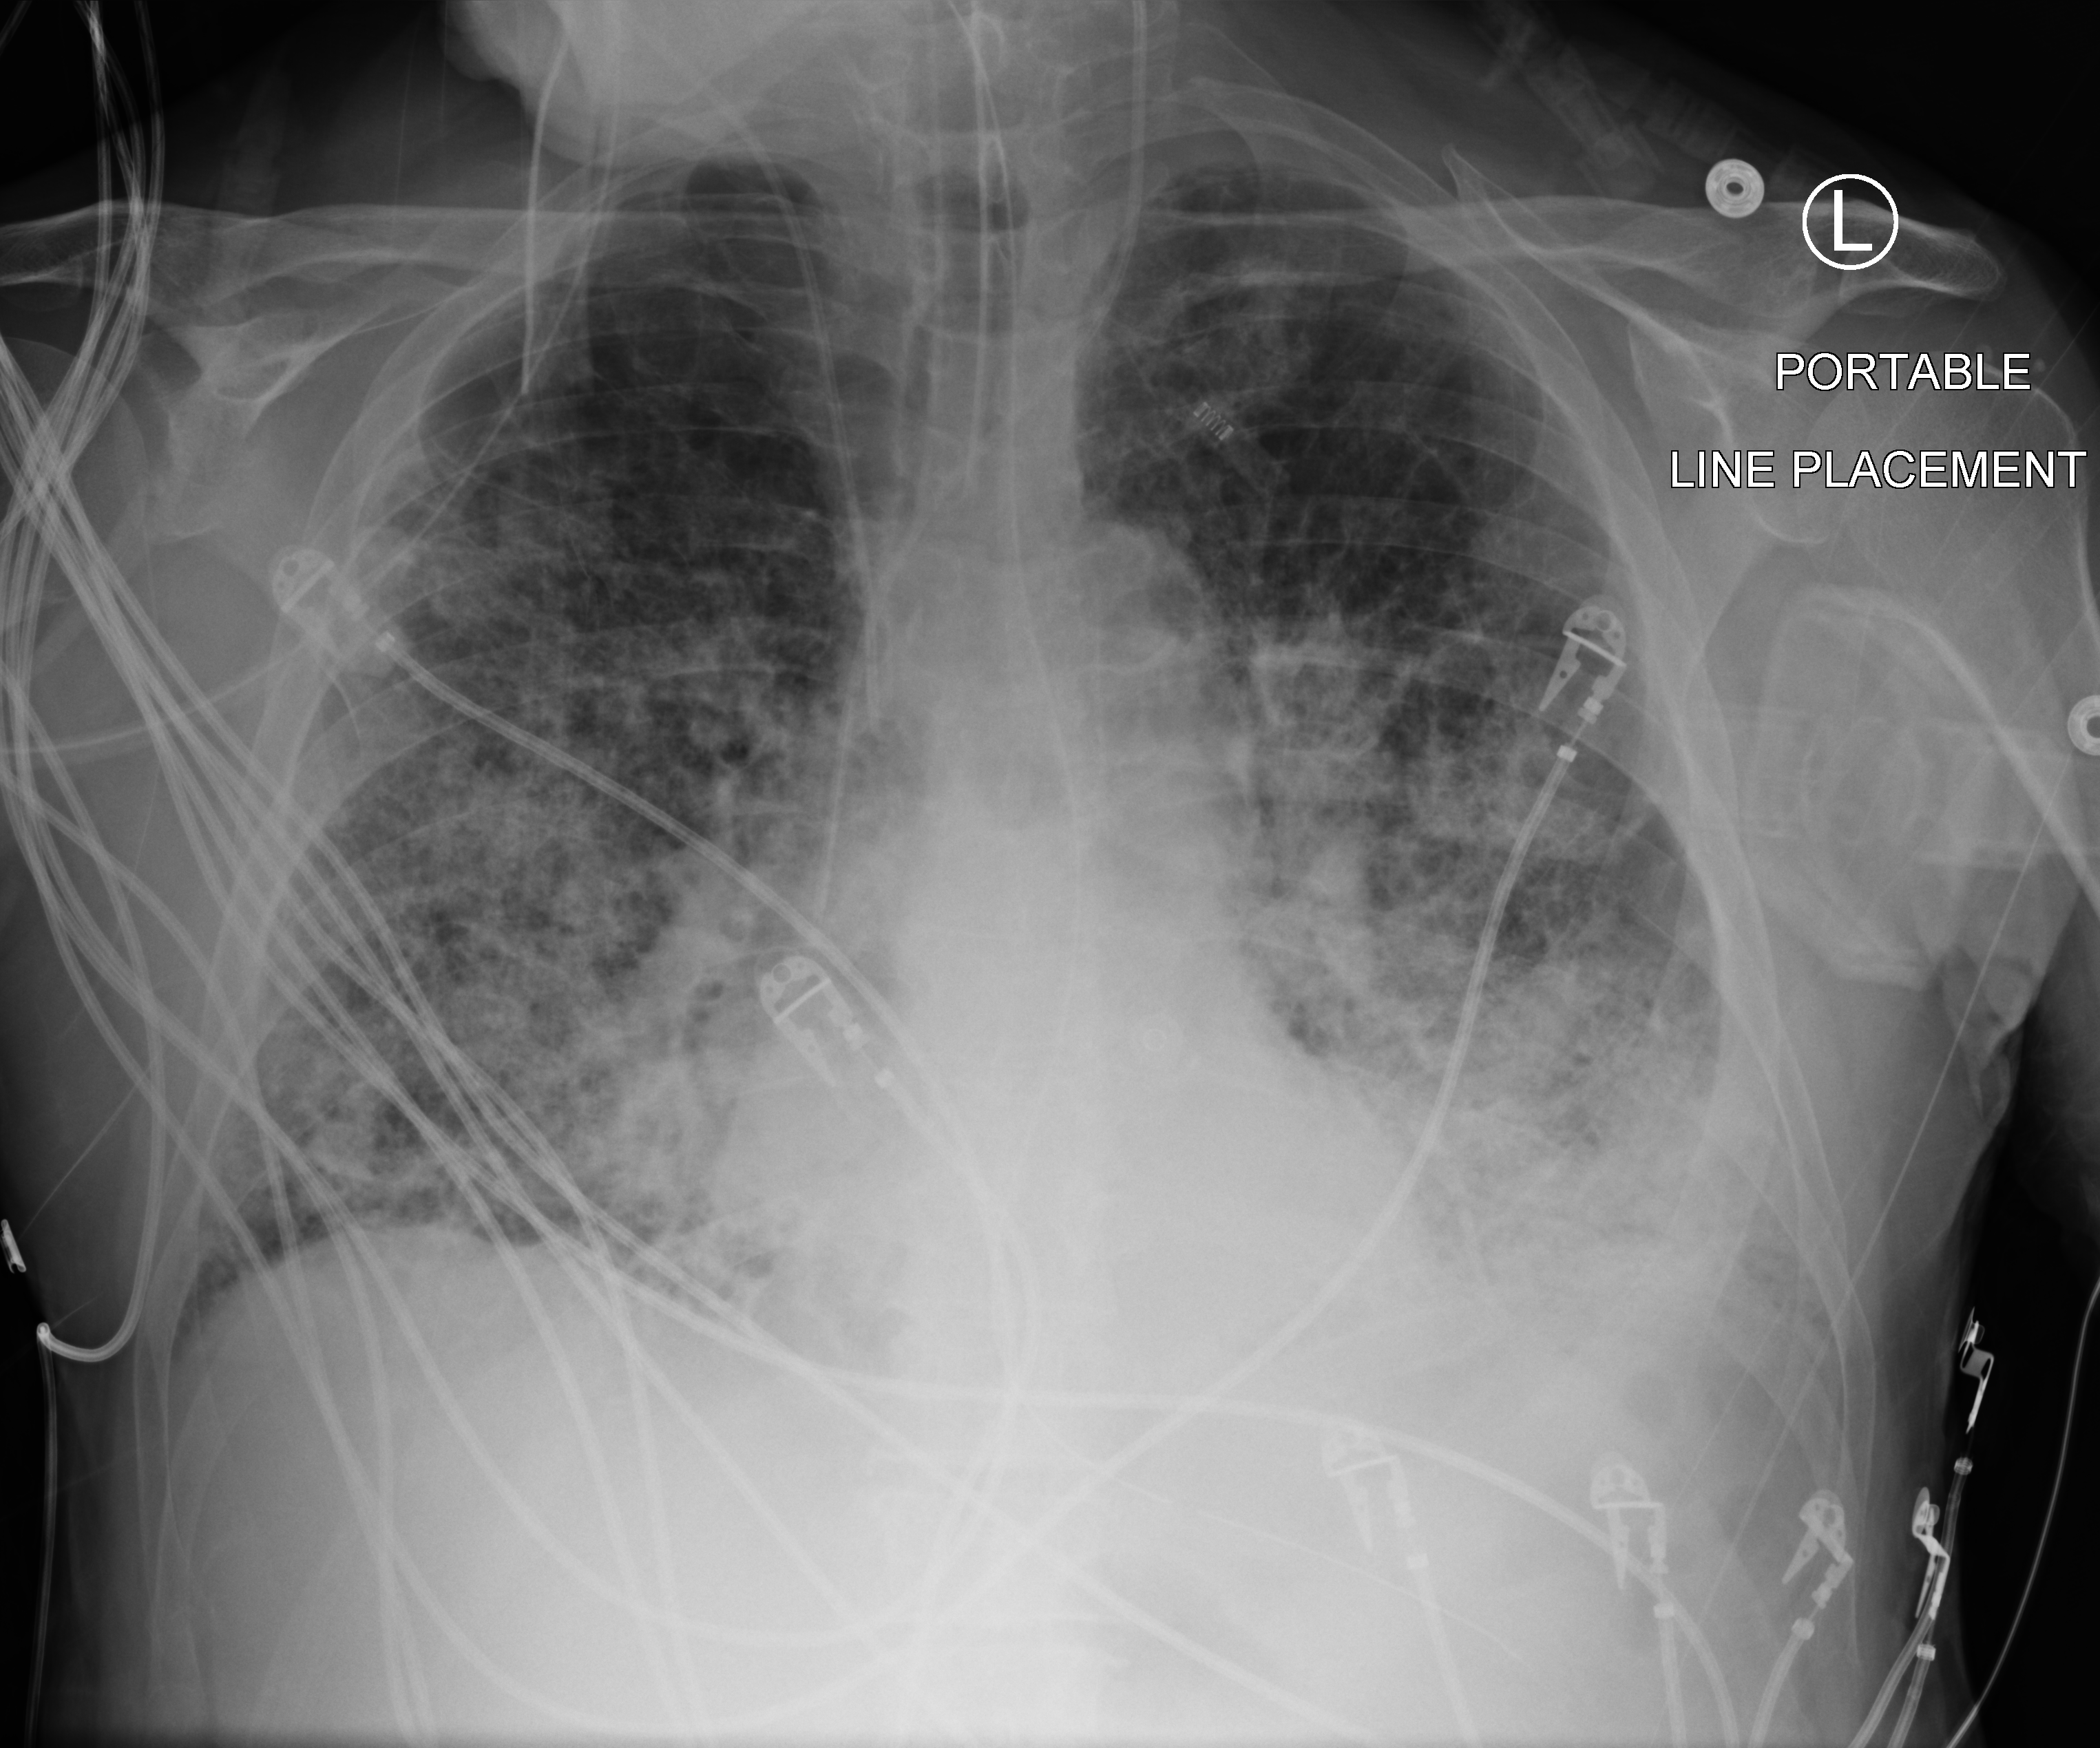
Bedside chest radiograph (computed radiography); anteroposterior (AP) projection. Patient hospitalised with COVID-19; male, aged 75–90 years.
From the hospital-stay record, not from the radiograph (when in the stay this image was taken is not recorded):
- admitted to intensive care during this hospital stay: yes